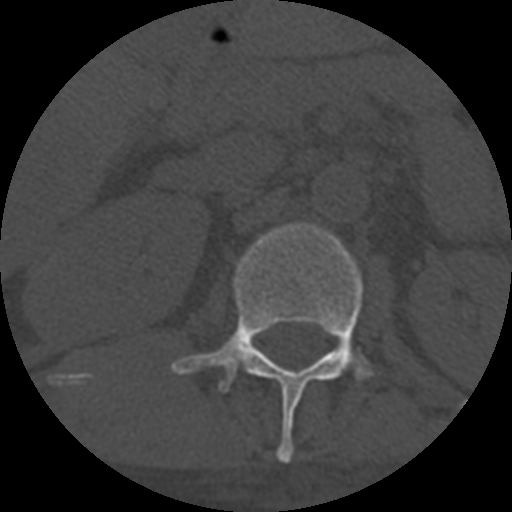
CT including the spine, one axial slice. One of 3 acquisitions stored at this slice position. Bone window (W 1800 / L 400 HU). 1.25 mm slice thickness. 512 × 512 image matrix, field of view 160 × 160 mm. Patient age 55 years. Case-level facts recorded for this patient, not image findings: primary cancer: colon.
Outlined on this slice (semi-automatically segmented with operator editing):
- L1 vertebra: bounding box <171,223,403,463> (left, top, right, bottom; pixels)